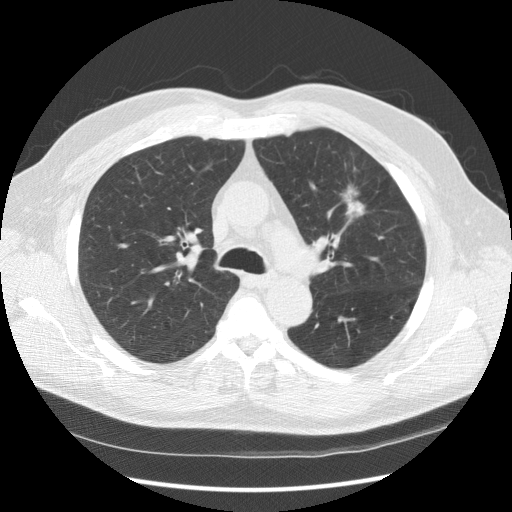
Low-dose screening chest CT, axial slice. Second annual screen. Lung window (W 1500 / L -600 HU). 120 kVp. Slice 54 of 157 in the series. 512 × 512 image matrix, field of view 370 × 370 mm. Male, age 65 years at enrolment.
• Expert reader's lesion annotation, bounding box [x1, y1, x2, y2] px = [324, 170, 379, 232].
• The screening reader recorded 2 non-calcified nodules or masses ≥4 mm on this exam (left upper lobe, right upper lobe); which of them this box marks is not recorded.
• Official screen result: positive, other.
• Lung cancer was diagnosed 120 days after this screen: carcinoma, NOS, left upper lobe, poorly differentiated (G3), stage IIIA (AJCC 6th edition), 25 mm at pathology.